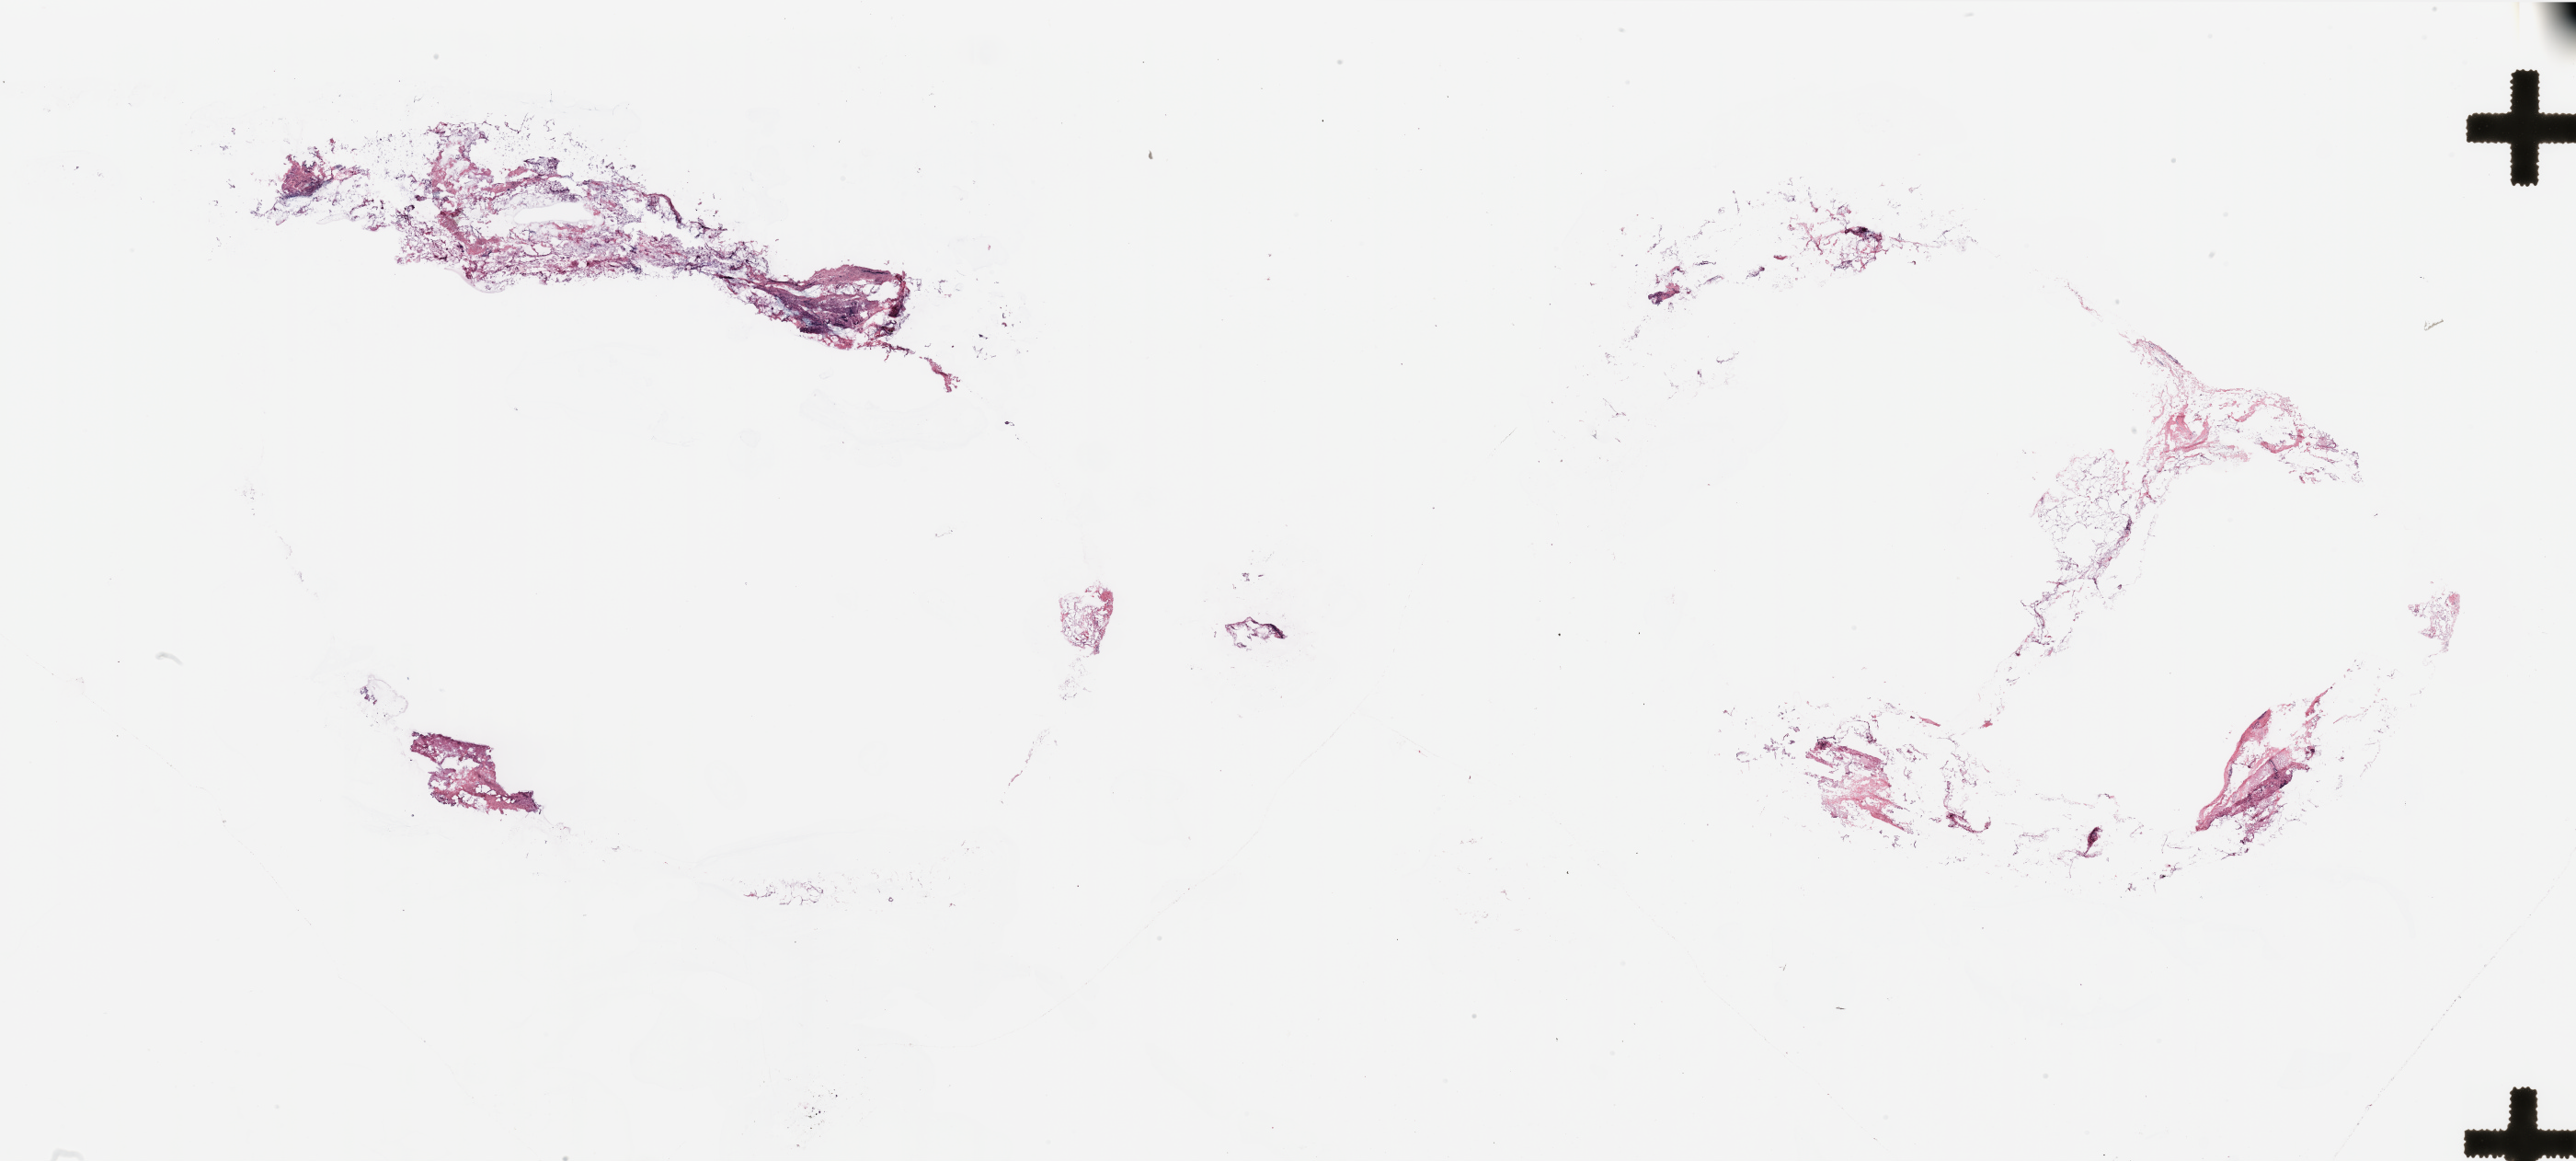
Hematoxylin and eosin (H&E) stained whole-slide image, shown as a low-resolution overview of the whole scanned area (about 44.3 x 20.0 mm, acquisition: 20x scan), breast, tumour tissue. 55-year-old female patient.
AJCC pathologic stage: IIA. Histologic diagnosis: Infiltrating duct carcinoma, NOS.